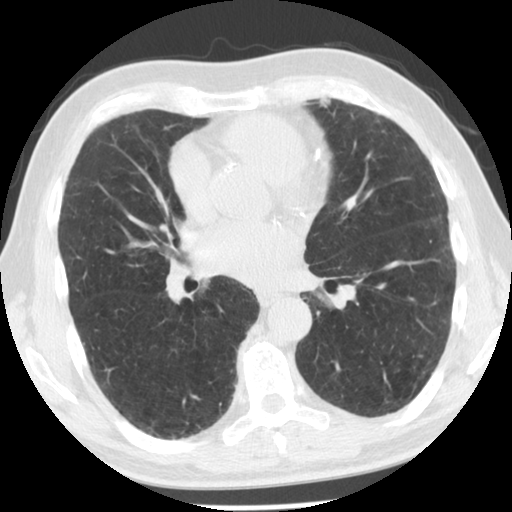
Chest CT (low-dose screening protocol), one axial image, second screening round (one year after baseline), lung window (W 1500 / L -600 HU), slice 62 of 129 in the series, 512 × 512 image matrix. Male participant, aged 66 years at enrolment. Former smoker at enrolment.
• Lesion marked by an expert reader, bounding box [x1, y1, x2, y2] px = [305, 88, 349, 129].
• The exam's reader record, not a measurement of the box and not confirmed to be the same lesion: non-calcified nodule or mass ≥4 mm, lingula, 6 × 5 mm, smooth margins, soft tissue attenuation, pre-existing on the prior screen: yes; interval growth: yes.
• Later outcome: lung cancer diagnosed 148 days after this screen — adenocarcinoma, NOS, left upper lobe, moderately differentiated (G2), stage IIB (AJCC 6th edition), 9 mm at pathology.